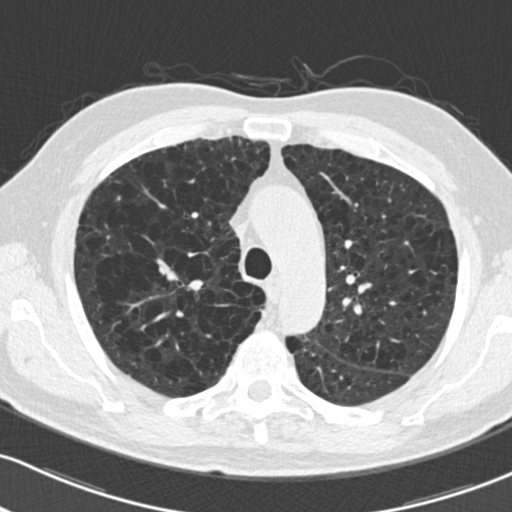
Low-dose screening chest CT, one axial slice. Position 151 of 204 along the scan axis. Lung window (W 1500 / L -600 HU). 512 × 512 image matrix, field of view 318 × 318 mm.
Structures marked on this image (expert manual segmentation):
- lesion 1 (tumor, upper lobe of right lung): bounding box (x1, y1, x2, y2) in pixels: (157, 258, 178, 281)